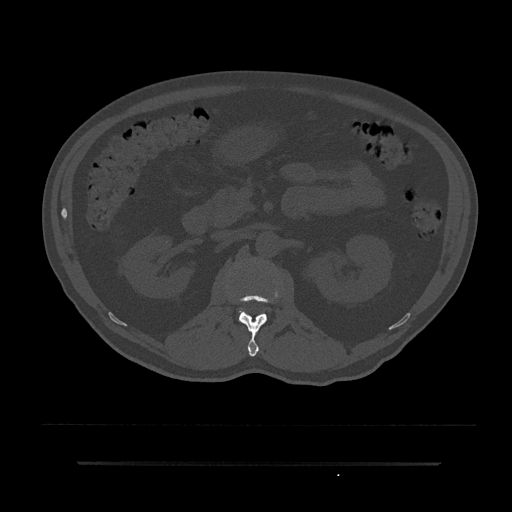
CT including the spine, one axial slice; slice 119 of 797 in the series (ordered by position); reconstruction kernel Br40s/3; 120 kVp; bone window (W 1800 / L 400 HU); 512 × 512 image matrix, field of view 464 × 464 mm. Male patient, age 59 years. Case-level facts recorded for this patient, not image findings: primary cancer: bile ducts.
Annotated regions visible in this slice (semi-automatic segmentation, software-assisted and operator-edited):
- L1 vertebra: bounding box <236,277,280,357> (left, top, right, bottom; pixels)
- L2 vertebra: <239,311,243,316>